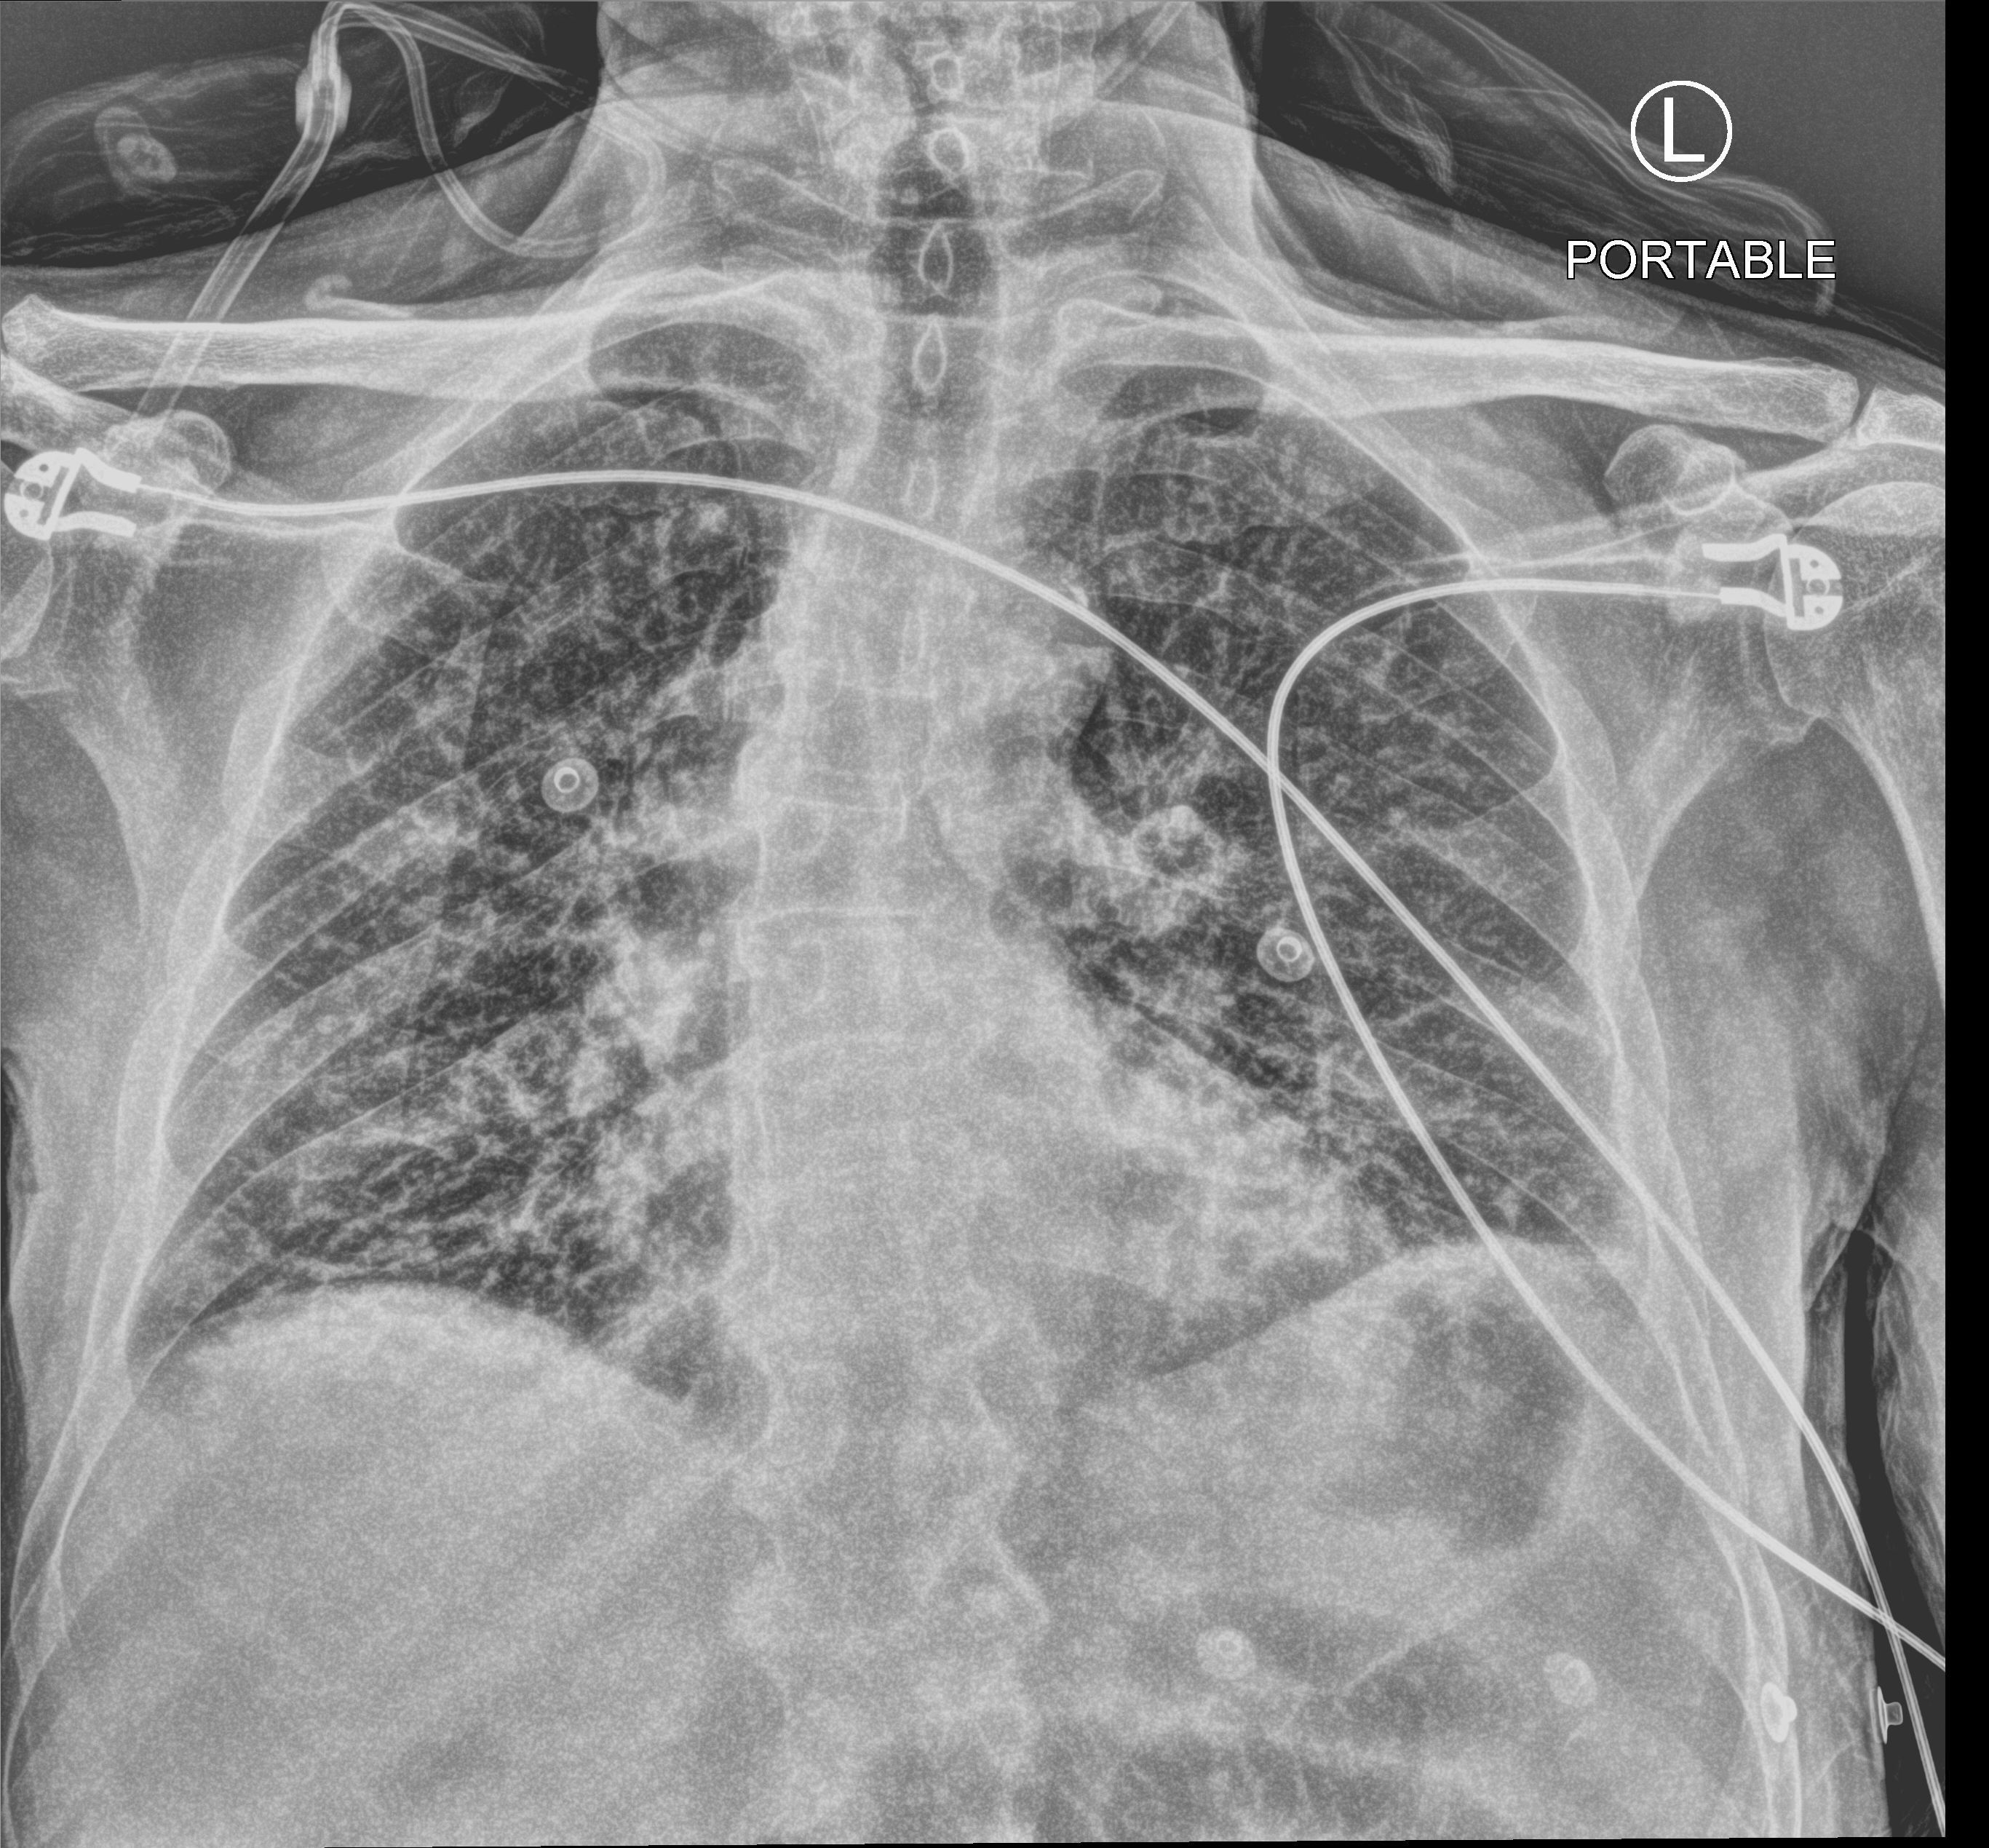
Chest X-ray (portable); anteroposterior (AP) projection. Male patient hospitalised with COVID-19, age 75–90 years.
Hospital-stay facts (about this admission, not read from this image; timing relative to this image not recorded): admitted to intensive care during this hospital stay: no; hypertension (admission record): yes; mechanically ventilated during this hospital stay: no.